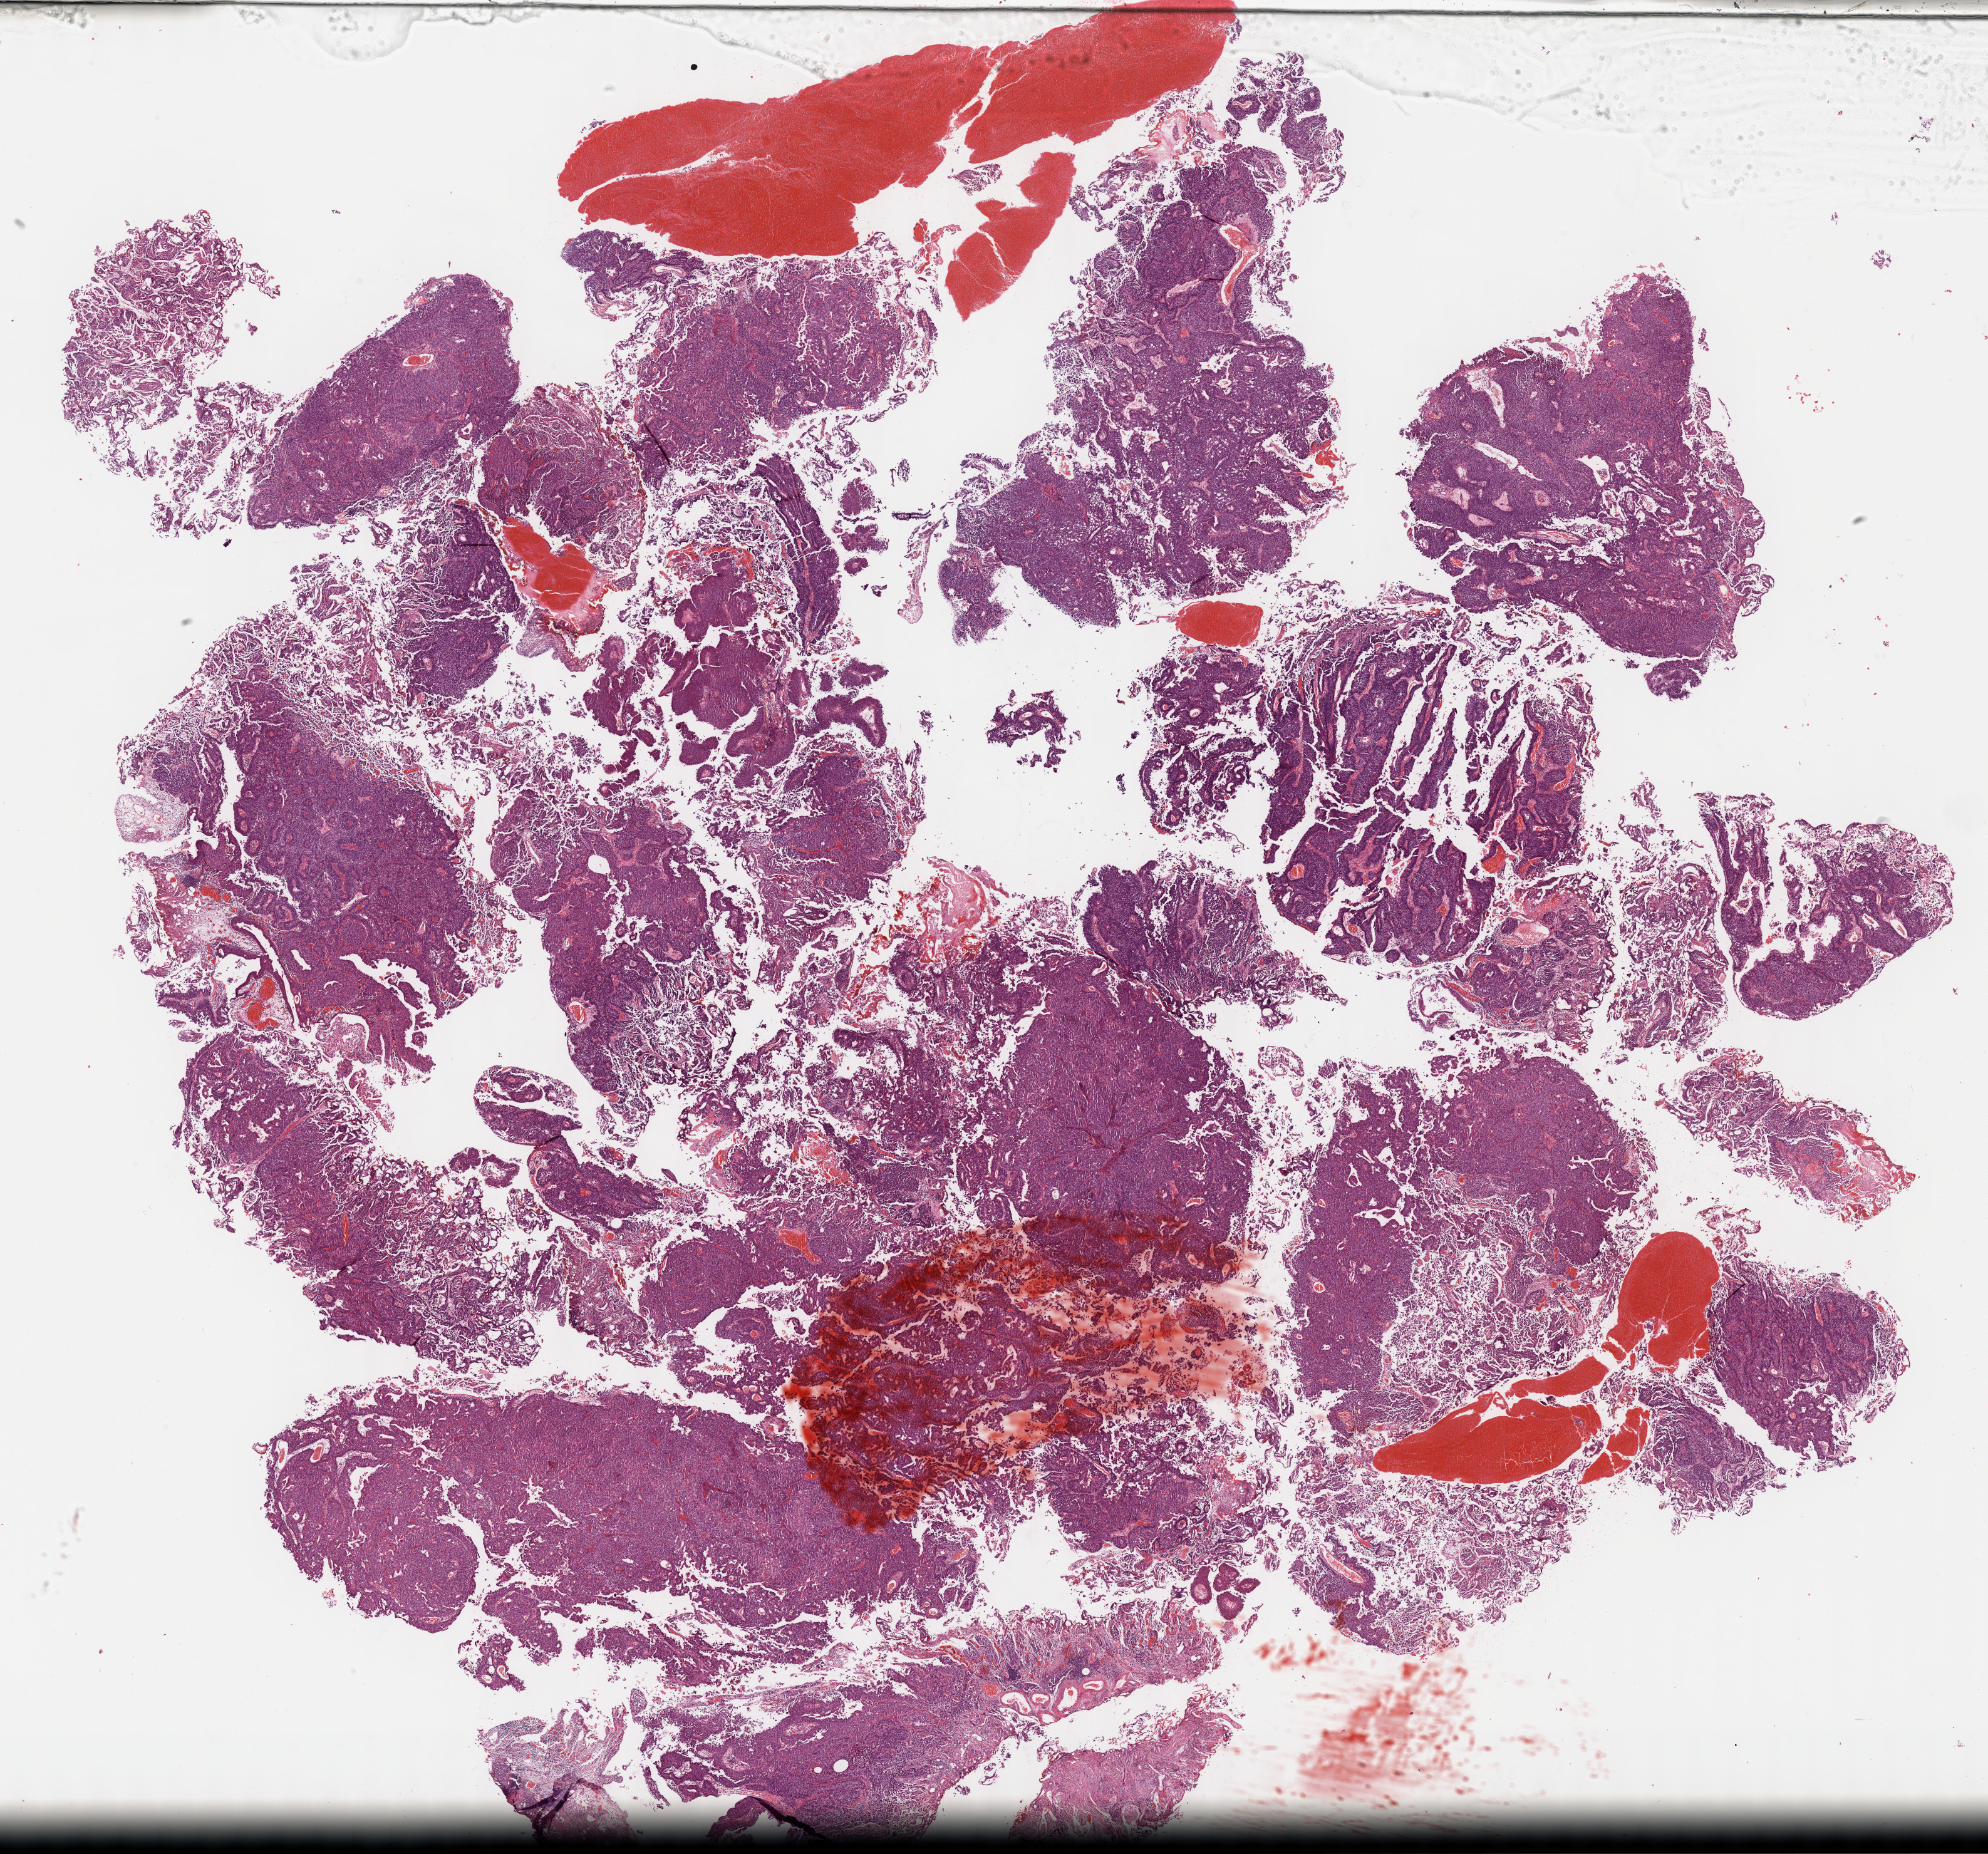
Whole-slide histology image, Hematoxylin and eosin (H&E) stained, whole scanned area (about 25.7 x 23.9 mm) shown as a low-resolution overview; formalin-fixed paraffin-embedded (FFPE) diagnostic section; bladder, primary tumour sample. Male, age 83 years at initial diagnosis. Histologic grade: high grade.
- diagnosis: Transitional cell carcinoma
- AJCC pathologic stage: II